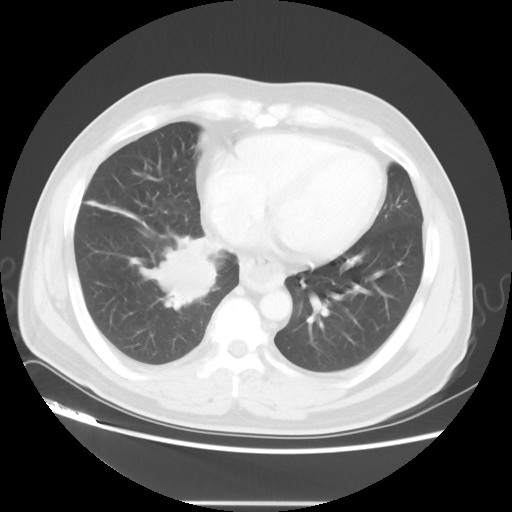
Chest CT, one axial slice. Position 18 of 48 along the scan axis. Reconstruction kernel STANDARD. 120 kVp. Lung window (W 1500 / L -600 HU). 5 mm slice thickness. 512 × 512 image matrix, field of view 390 × 390 mm. Patient: male, 53 years. From the clinical record (not read from this slice): clinical TNM (as recorded): T2 N3 M0; histopathological grade: G3.
Structures marked on this image (rectangle marked by the reading radiologist):
- lung tumour (recorded histology: small cell carcinoma): bounding box [x1, y1, x2, y2] px = [142, 243, 223, 330]